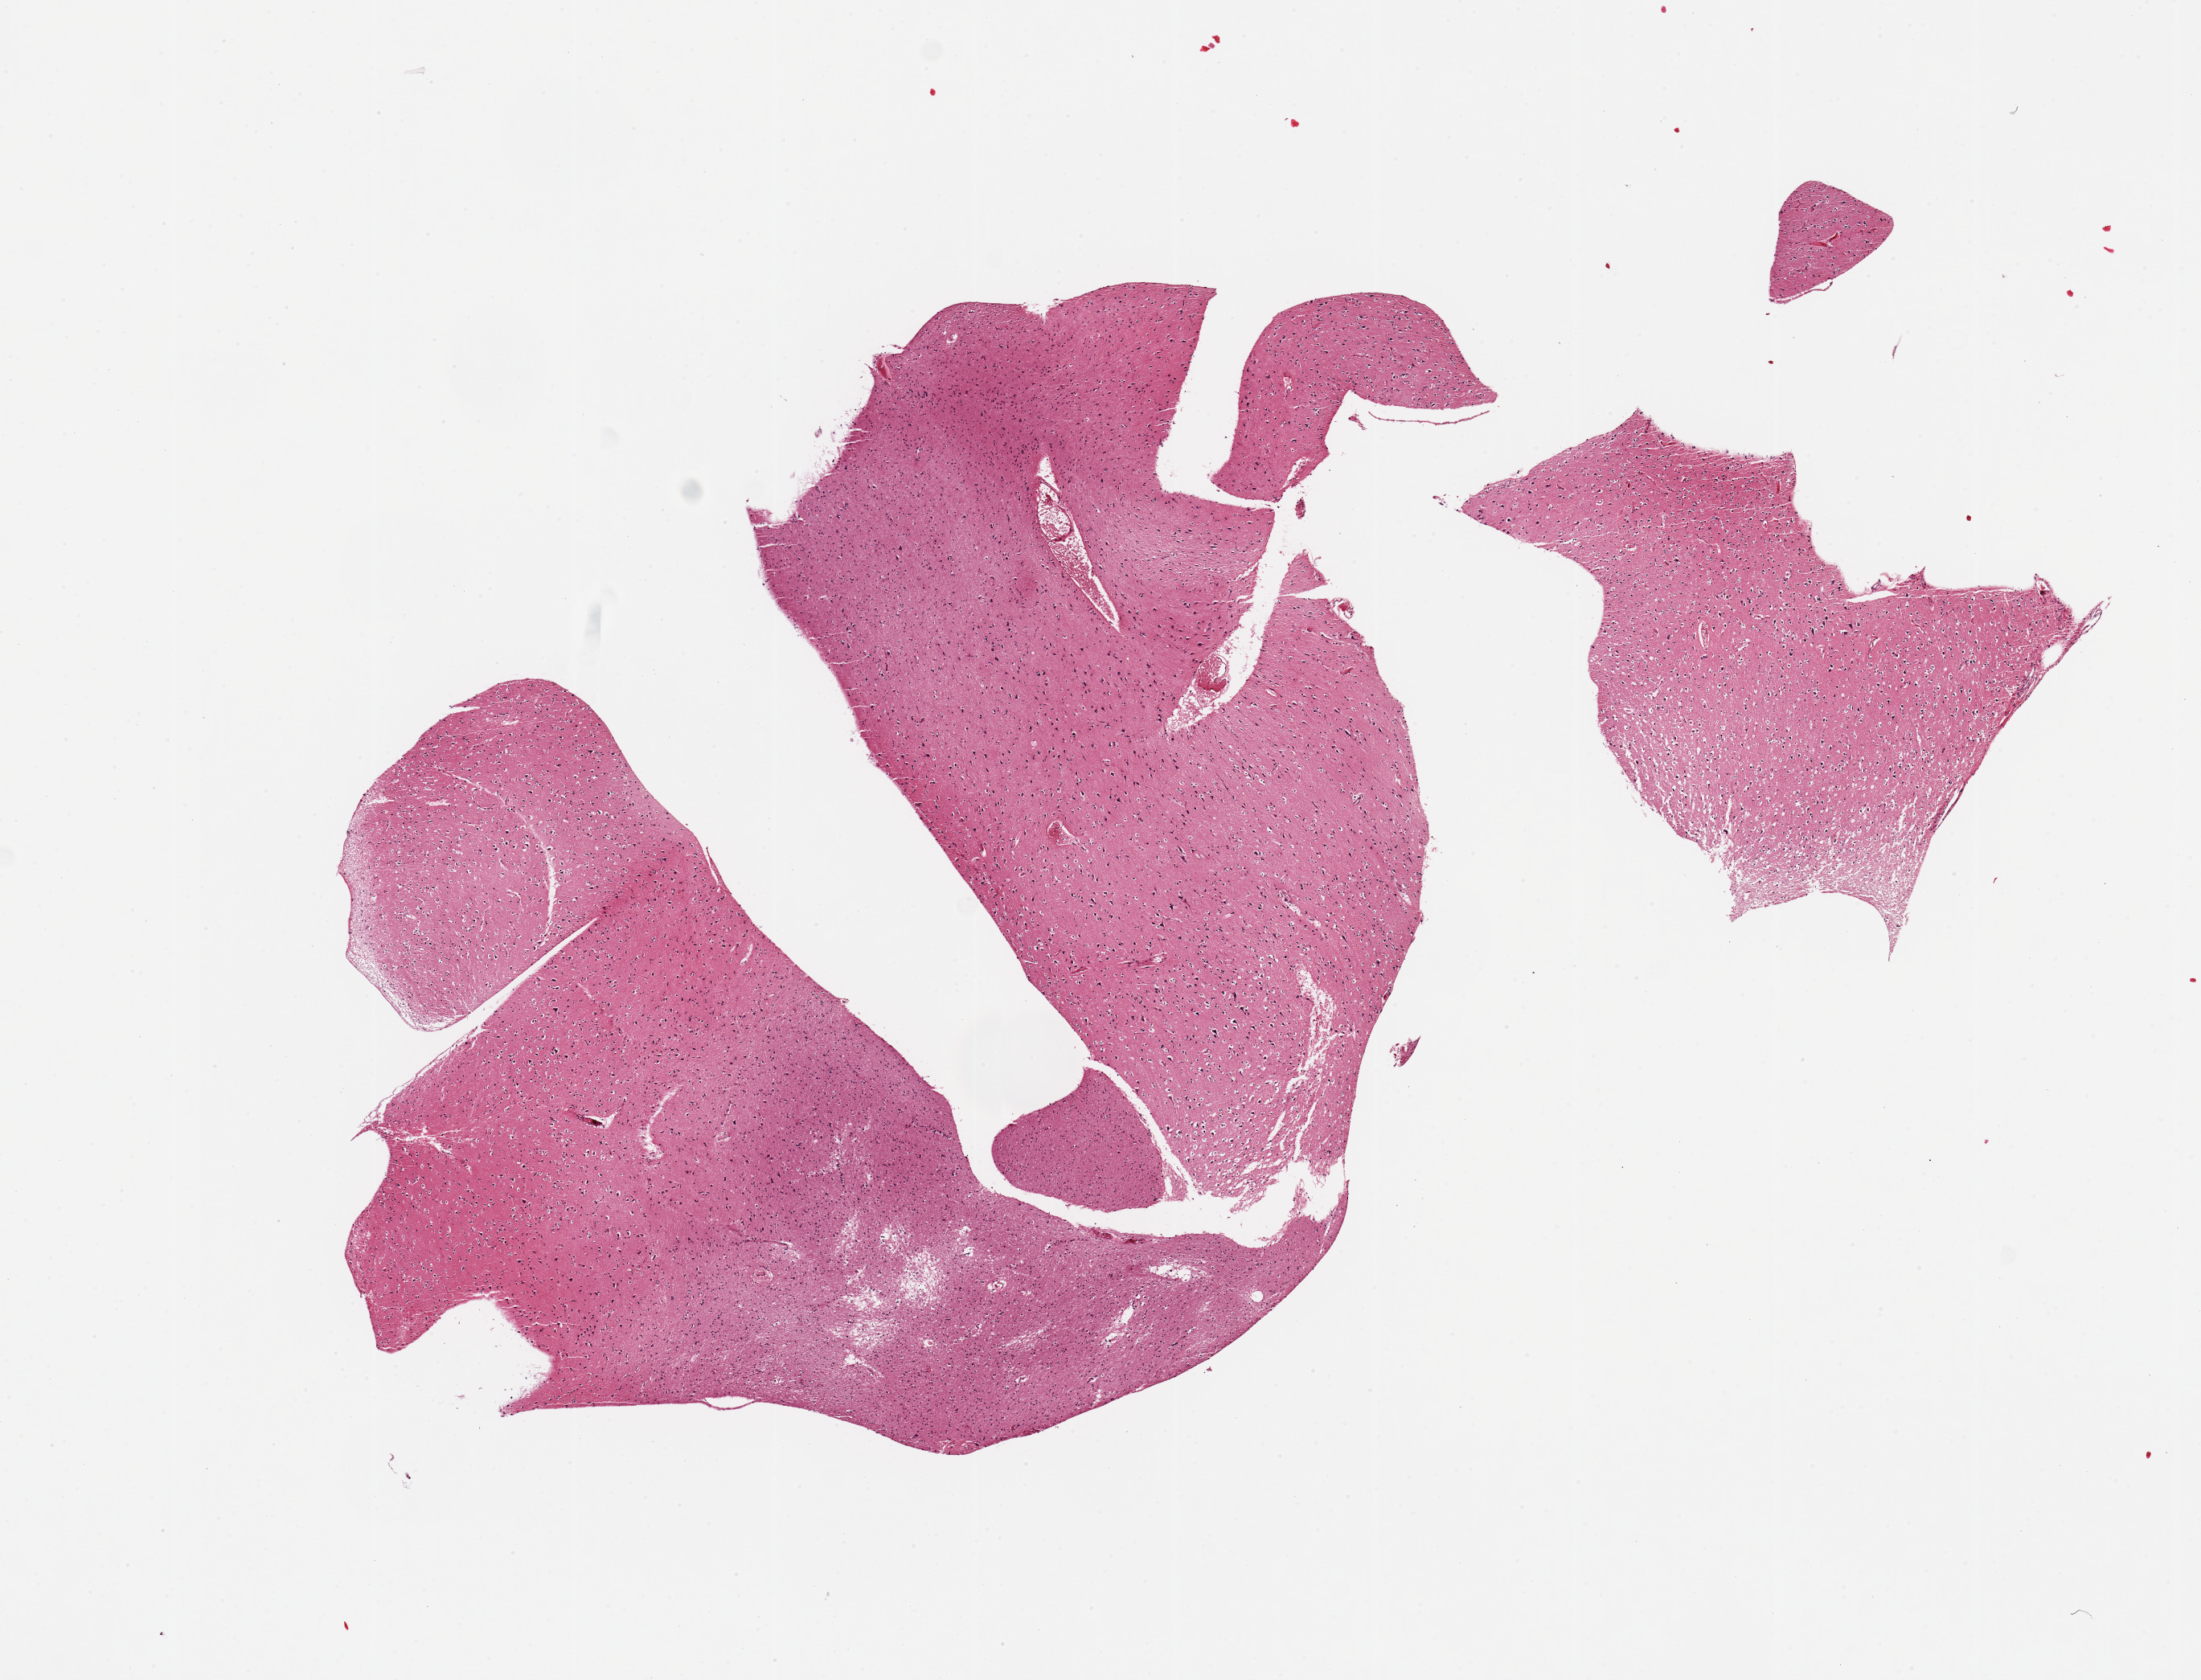
Digitized hematoxylin and eosin (H&E)-stained section — whole scanned area (about 10.8 x 8.3 mm) shown as a low-resolution overview, PAXgene-fixed, paraffin-embedded tissue, section of cerebral cortex (target tissue), donor tissue sample. Male donor.
Pathologist's review note for this sample: 2 pieces (fragmented).